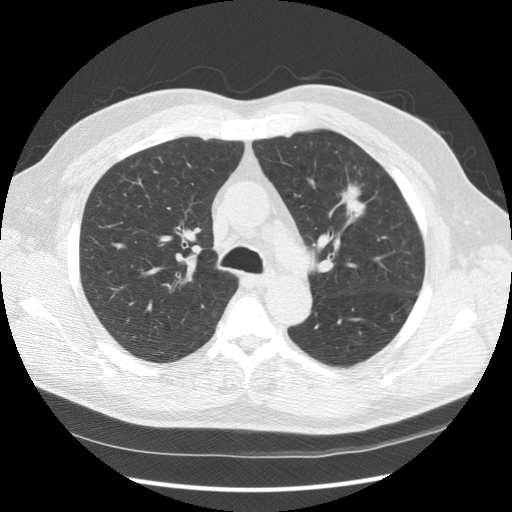
Low-dose screening chest CT, one axial slice; position 105 of 157 along the scan axis; 120 kVp; lung window (W 1500 / L -600 HU); 2.5 mm slice thickness; 512 × 512 image matrix, field of view 370 × 370 mm.
Annotated regions visible in this slice (manually delineated by an expert):
- lesion 1 (tumor, upper lobe of left lung): box from (x=342, y=185) to (x=365, y=220) px